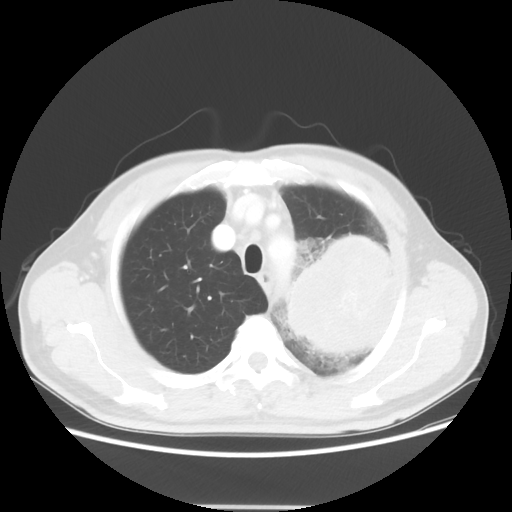
Chest CT, one axial slice; position 44 of 53 along the scan axis; 100 kVp; lung window (W 1500 / L -600 HU); 5 mm slice thickness; 512 × 512 image matrix, field of view 391 × 391 mm. Patient: male, 60 years. From the clinical record (not read from this slice): clinical TNM (as recorded): T4 N1 M1a.
Annotated regions visible in this slice (rectangle marked by the reading radiologist):
- lung tumour (recorded histology: large cell carcinoma): bounding box (x1, y1, x2, y2) in pixels: (274, 221, 400, 371)